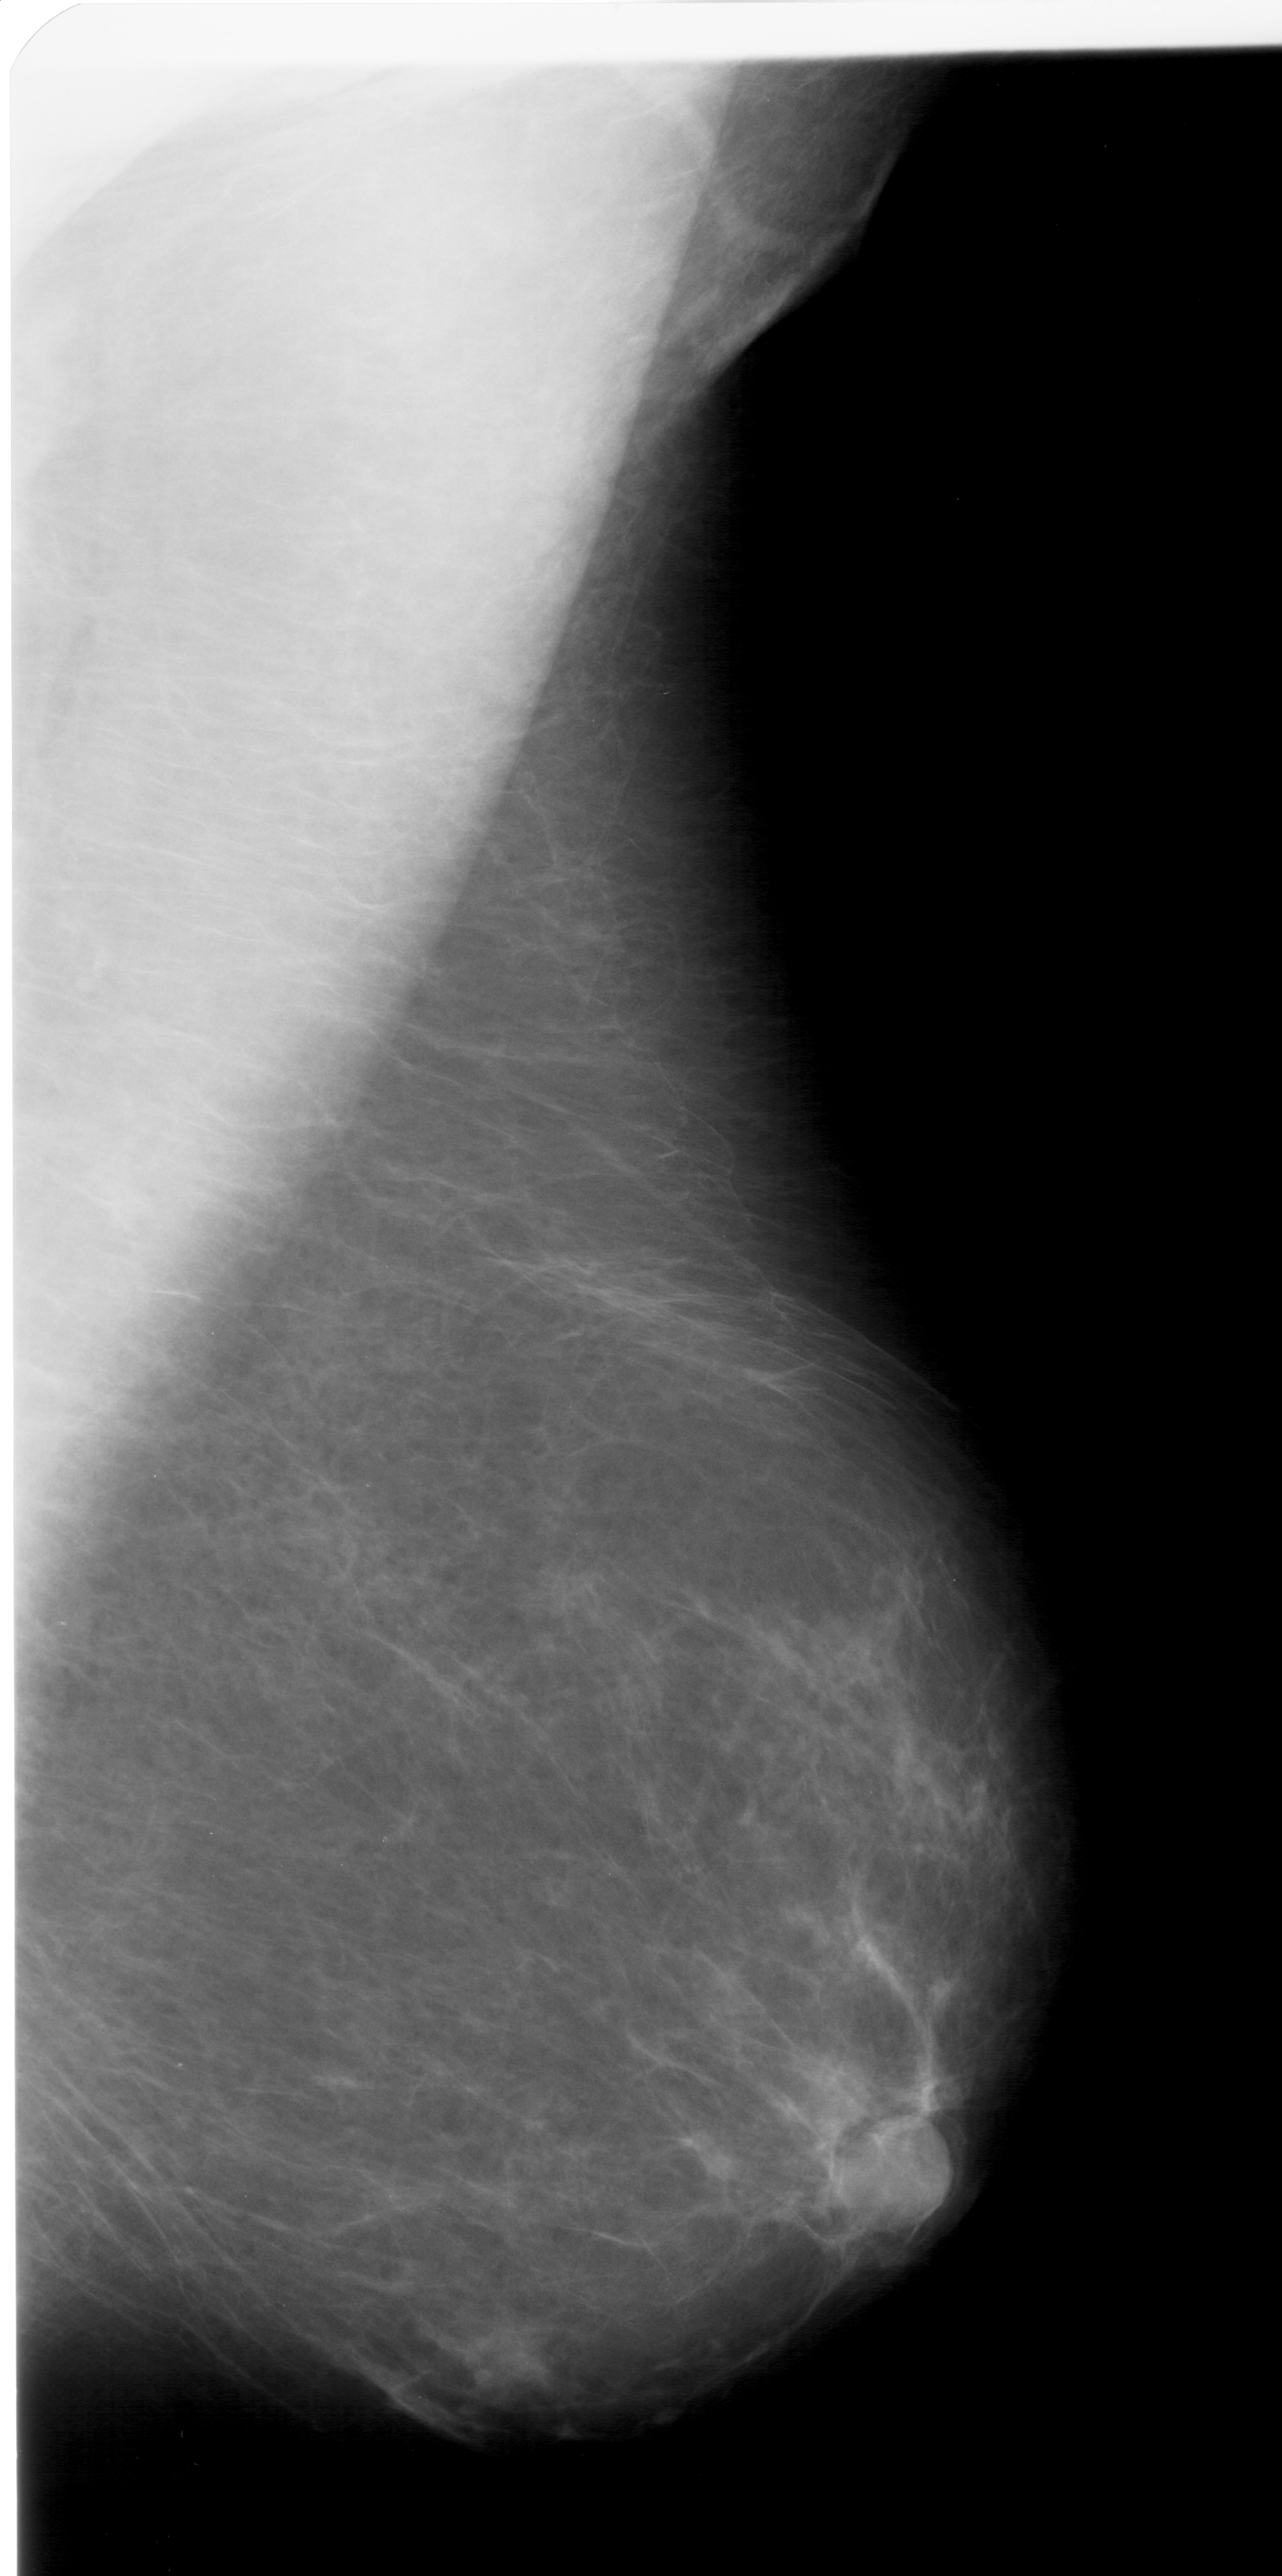
Digitized screen-film mammogram, right breast, MLO view, breast composition: scattered fibroglandular densities (BI-RADS density category 2 of 4).
Marked findings (only marked abnormalities are described; nothing is implied about the rest of the image): mass, shape irregular, margins ill defined; BI-RADS assessment category 4; pathology (as recorded): benign.